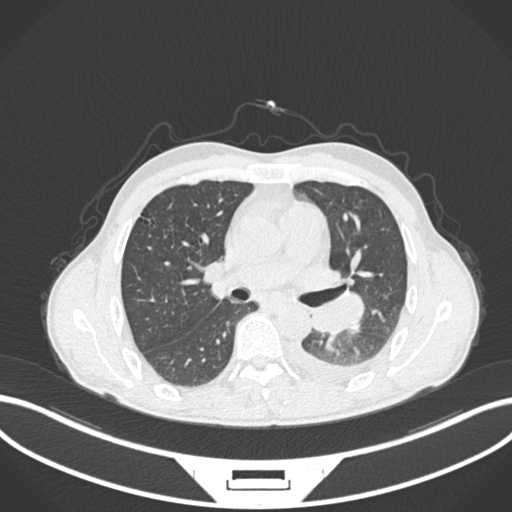
Chest CT, one axial slice; slice 141 of 222 in the series (ordered by position); reconstruction kernel B30f; lung window (W 1500 / L -600 HU); 1 mm slice thickness; 512 × 512 image matrix, field of view 400 × 400 mm. Male patient, age 47 years. Case-level facts recorded for this patient, not image findings: clinical TNM (as recorded): T3 N1 M1c.
Outlined on this slice (rectangle marked by the reading radiologist):
- lung tumour (recorded histology: small cell carcinoma): bounding box (x1, y1, x2, y2) in pixels: (307, 289, 366, 336)